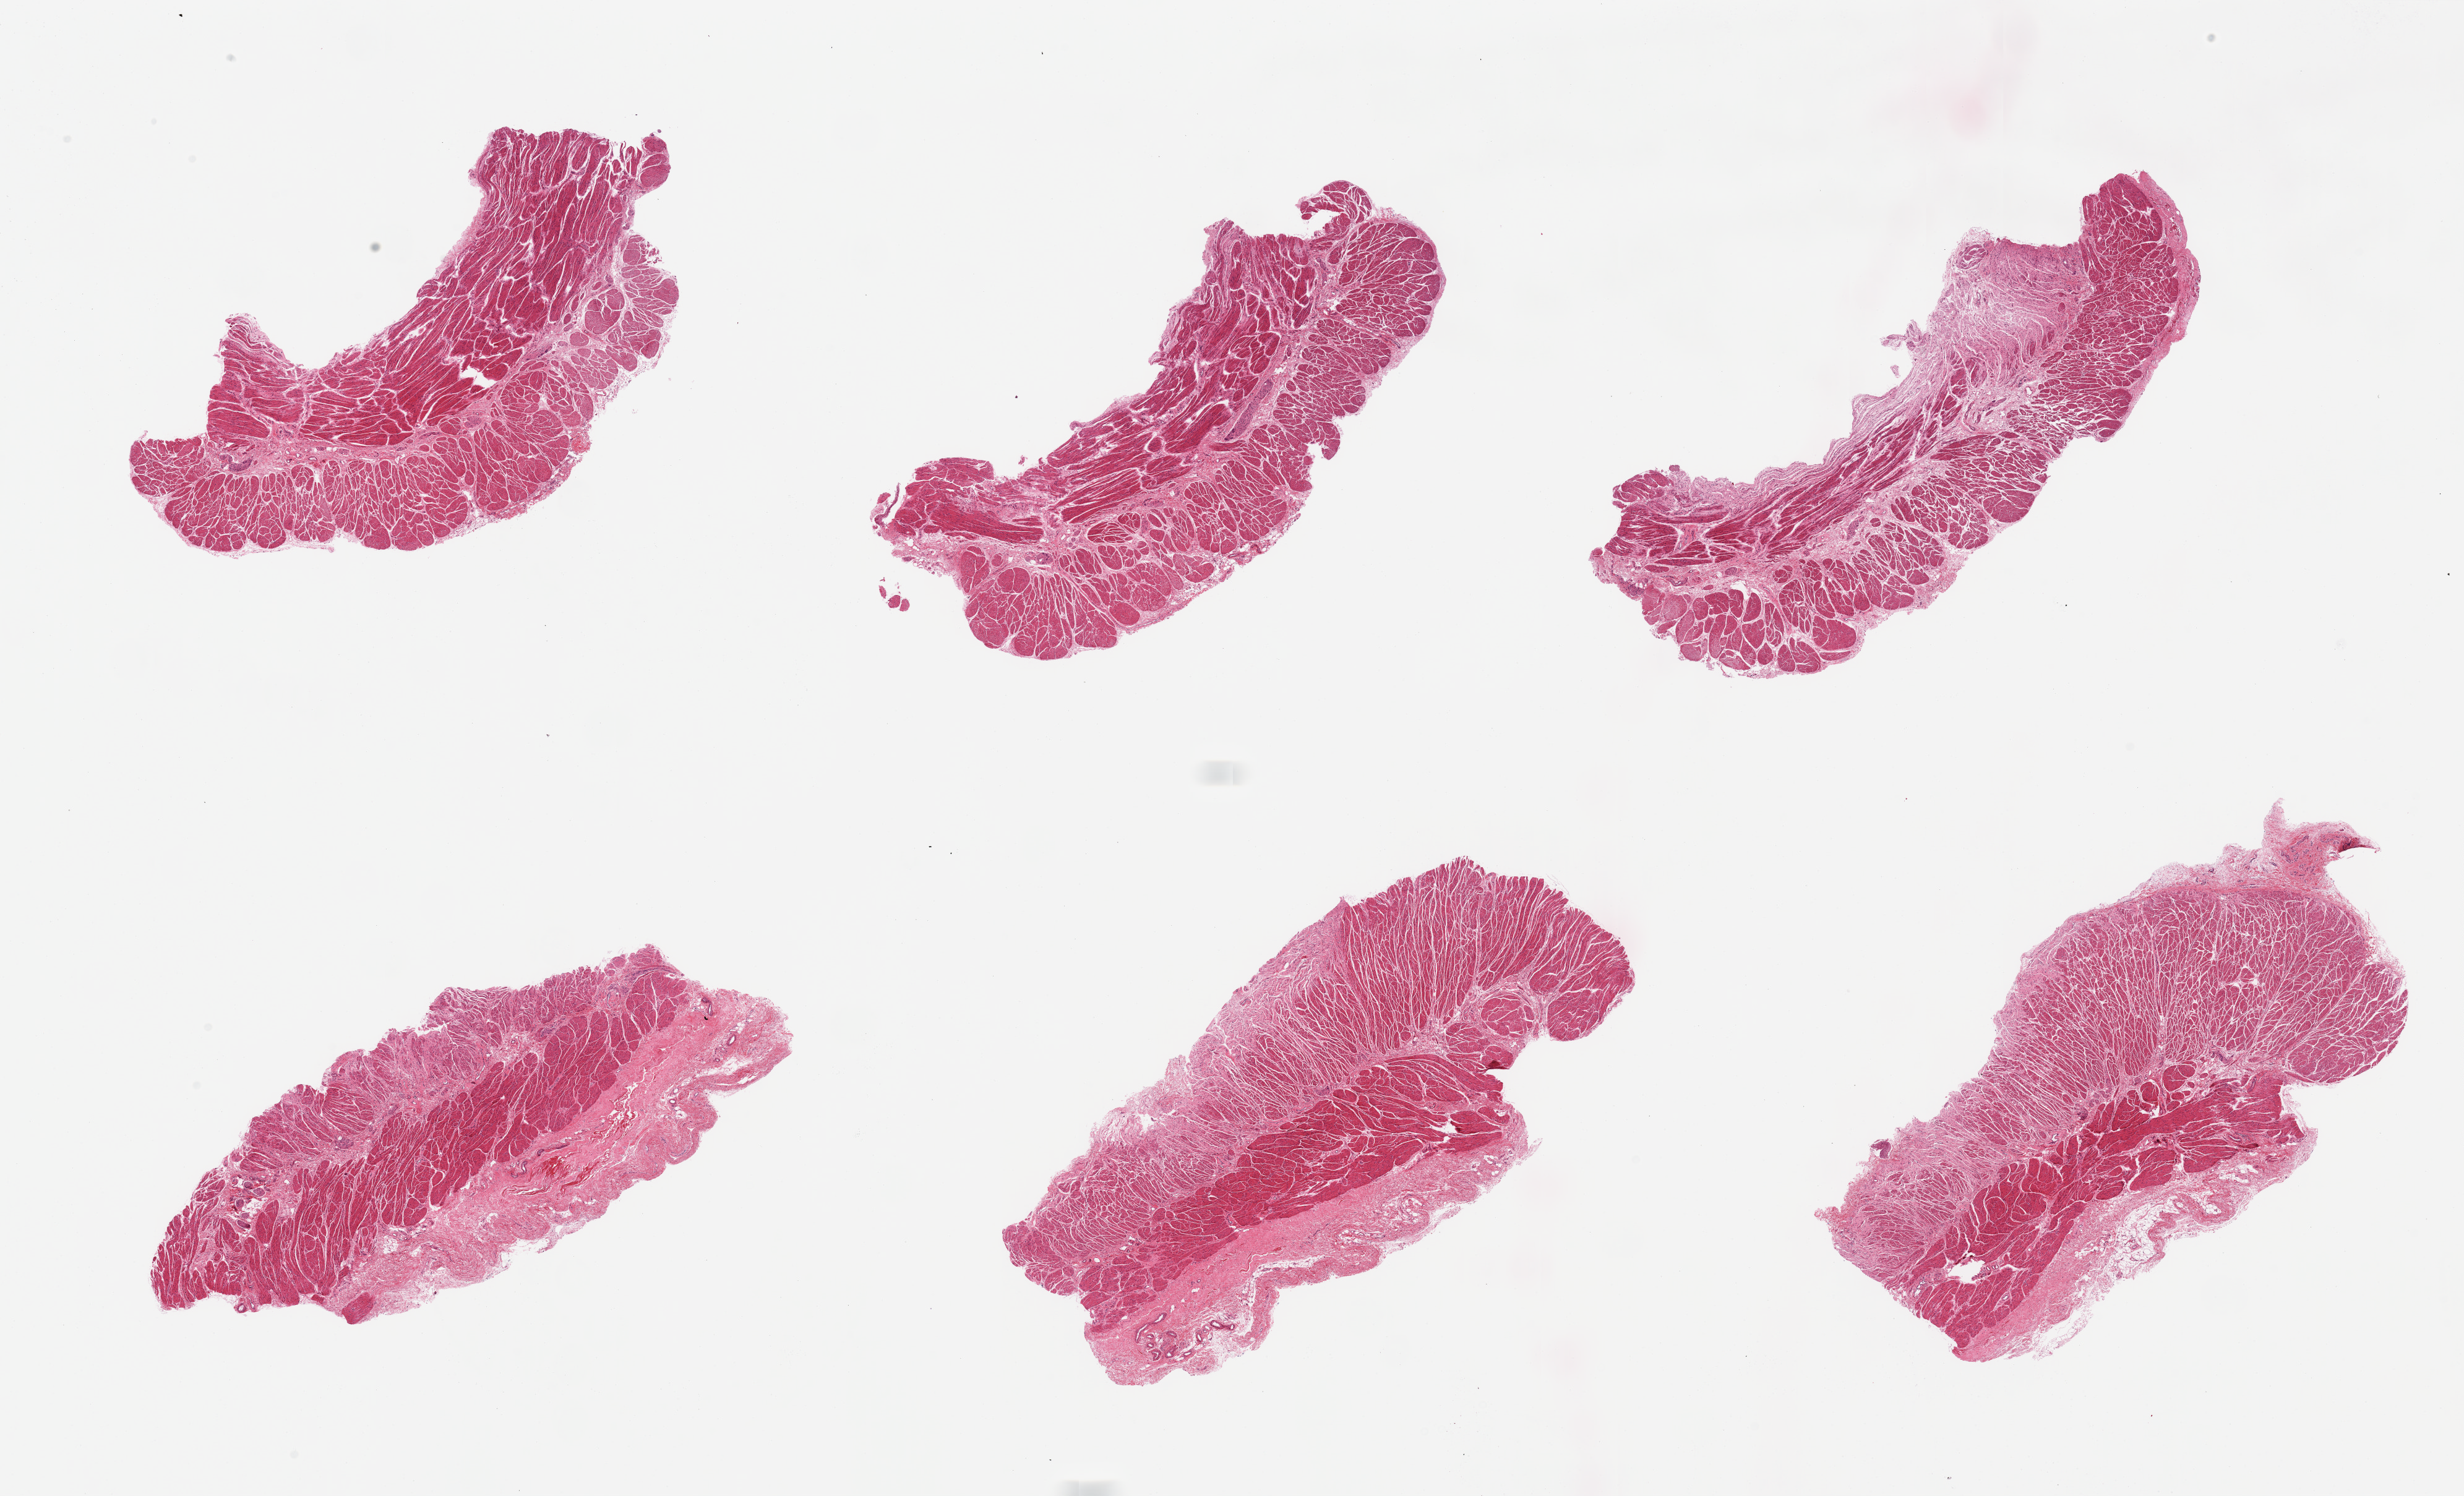
Whole-slide image, haematoxylin and eosin stain, brightfield — whole scanned area (about 31.5 x 19.1 mm) shown as a low-resolution overview. PAXgene-fixed paraffin-embedded (PFPE) section. Sampled site (target tissue): gastroesophageal junction. Donor tissue sample. Donor sex: female.
Review note (as recorded): 6 pieces, all muscularis, good sepcimens.